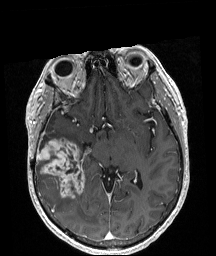
Brain MRI from a brain-tumour surgery series, one axial slice; position 112 of 208 along the scan axis; T1-weighted post-contrast; 1 mm slice thickness; 216 × 256 image matrix, field of view 211 × 250 mm. Case-level facts recorded for this patient, not image findings: histopathology: Astrocytoma; WHO grade: 4; IDH mutation: yes; tumour location: Right Temporal.
Annotated regions visible in this slice (manually delineated by an expert):
- tumour: bounding box (x1, y1, x2, y2) in pixels: (36, 139, 84, 198)